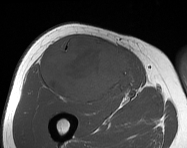
MRI of an extremity soft-tissue mass, one axial slice; slice 85 of 114 in the series (ordered by position); MR volume resampled by the dataset authors to the PET/CT grid (not the native acquisition matrix); 3.27 mm slice thickness; 187 × 148 image matrix, field of view 183 × 145 mm. Male patient. Case-level facts recorded for this patient, not image findings: histological type: pleiomorphic leiomyosarcoma; grade: intermediate; site of the primary tumour: right thigh.
Annotated regions visible in this slice (expert contour drawn on MRI and transferred to this co-registered scan by the dataset authors):
- gross tumour volume including surrounding oedema: box from (x=43, y=35) to (x=133, y=103) px
- gross tumour volume (mass): (x=43, y=35)–(x=133, y=103)